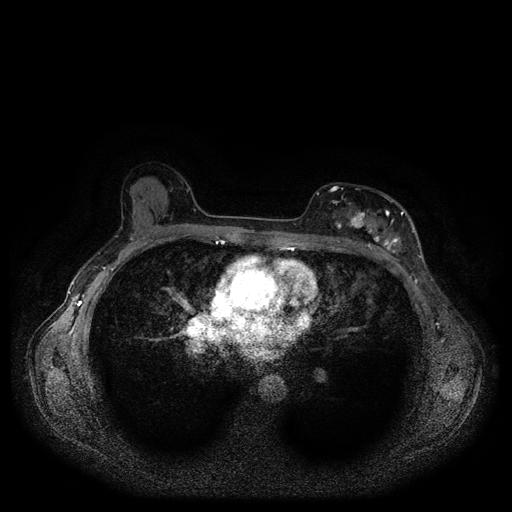
Breast MRI (dynamic contrast-enhanced, multi-phase), one axial slice. Slice 63 of 116 in the series (ordered by position). Dynamic contrast-enhanced series, time point 2 of 5 at this slice position (early post-contrast). 1.5 T. TE 2.6 ms, TR 5.3 ms. 2 mm slice thickness. 512 × 512 image matrix, field of view 350 × 350 mm. Patient: female, 51 years.
Outlined on this slice (semi-automatically segmented with operator editing):
- breast lesion (labelled 'tumour' in the annotation; benign lesions carry a separate 'benign' label): bounding box <324,204,397,248> (left, top, right, bottom; pixels)